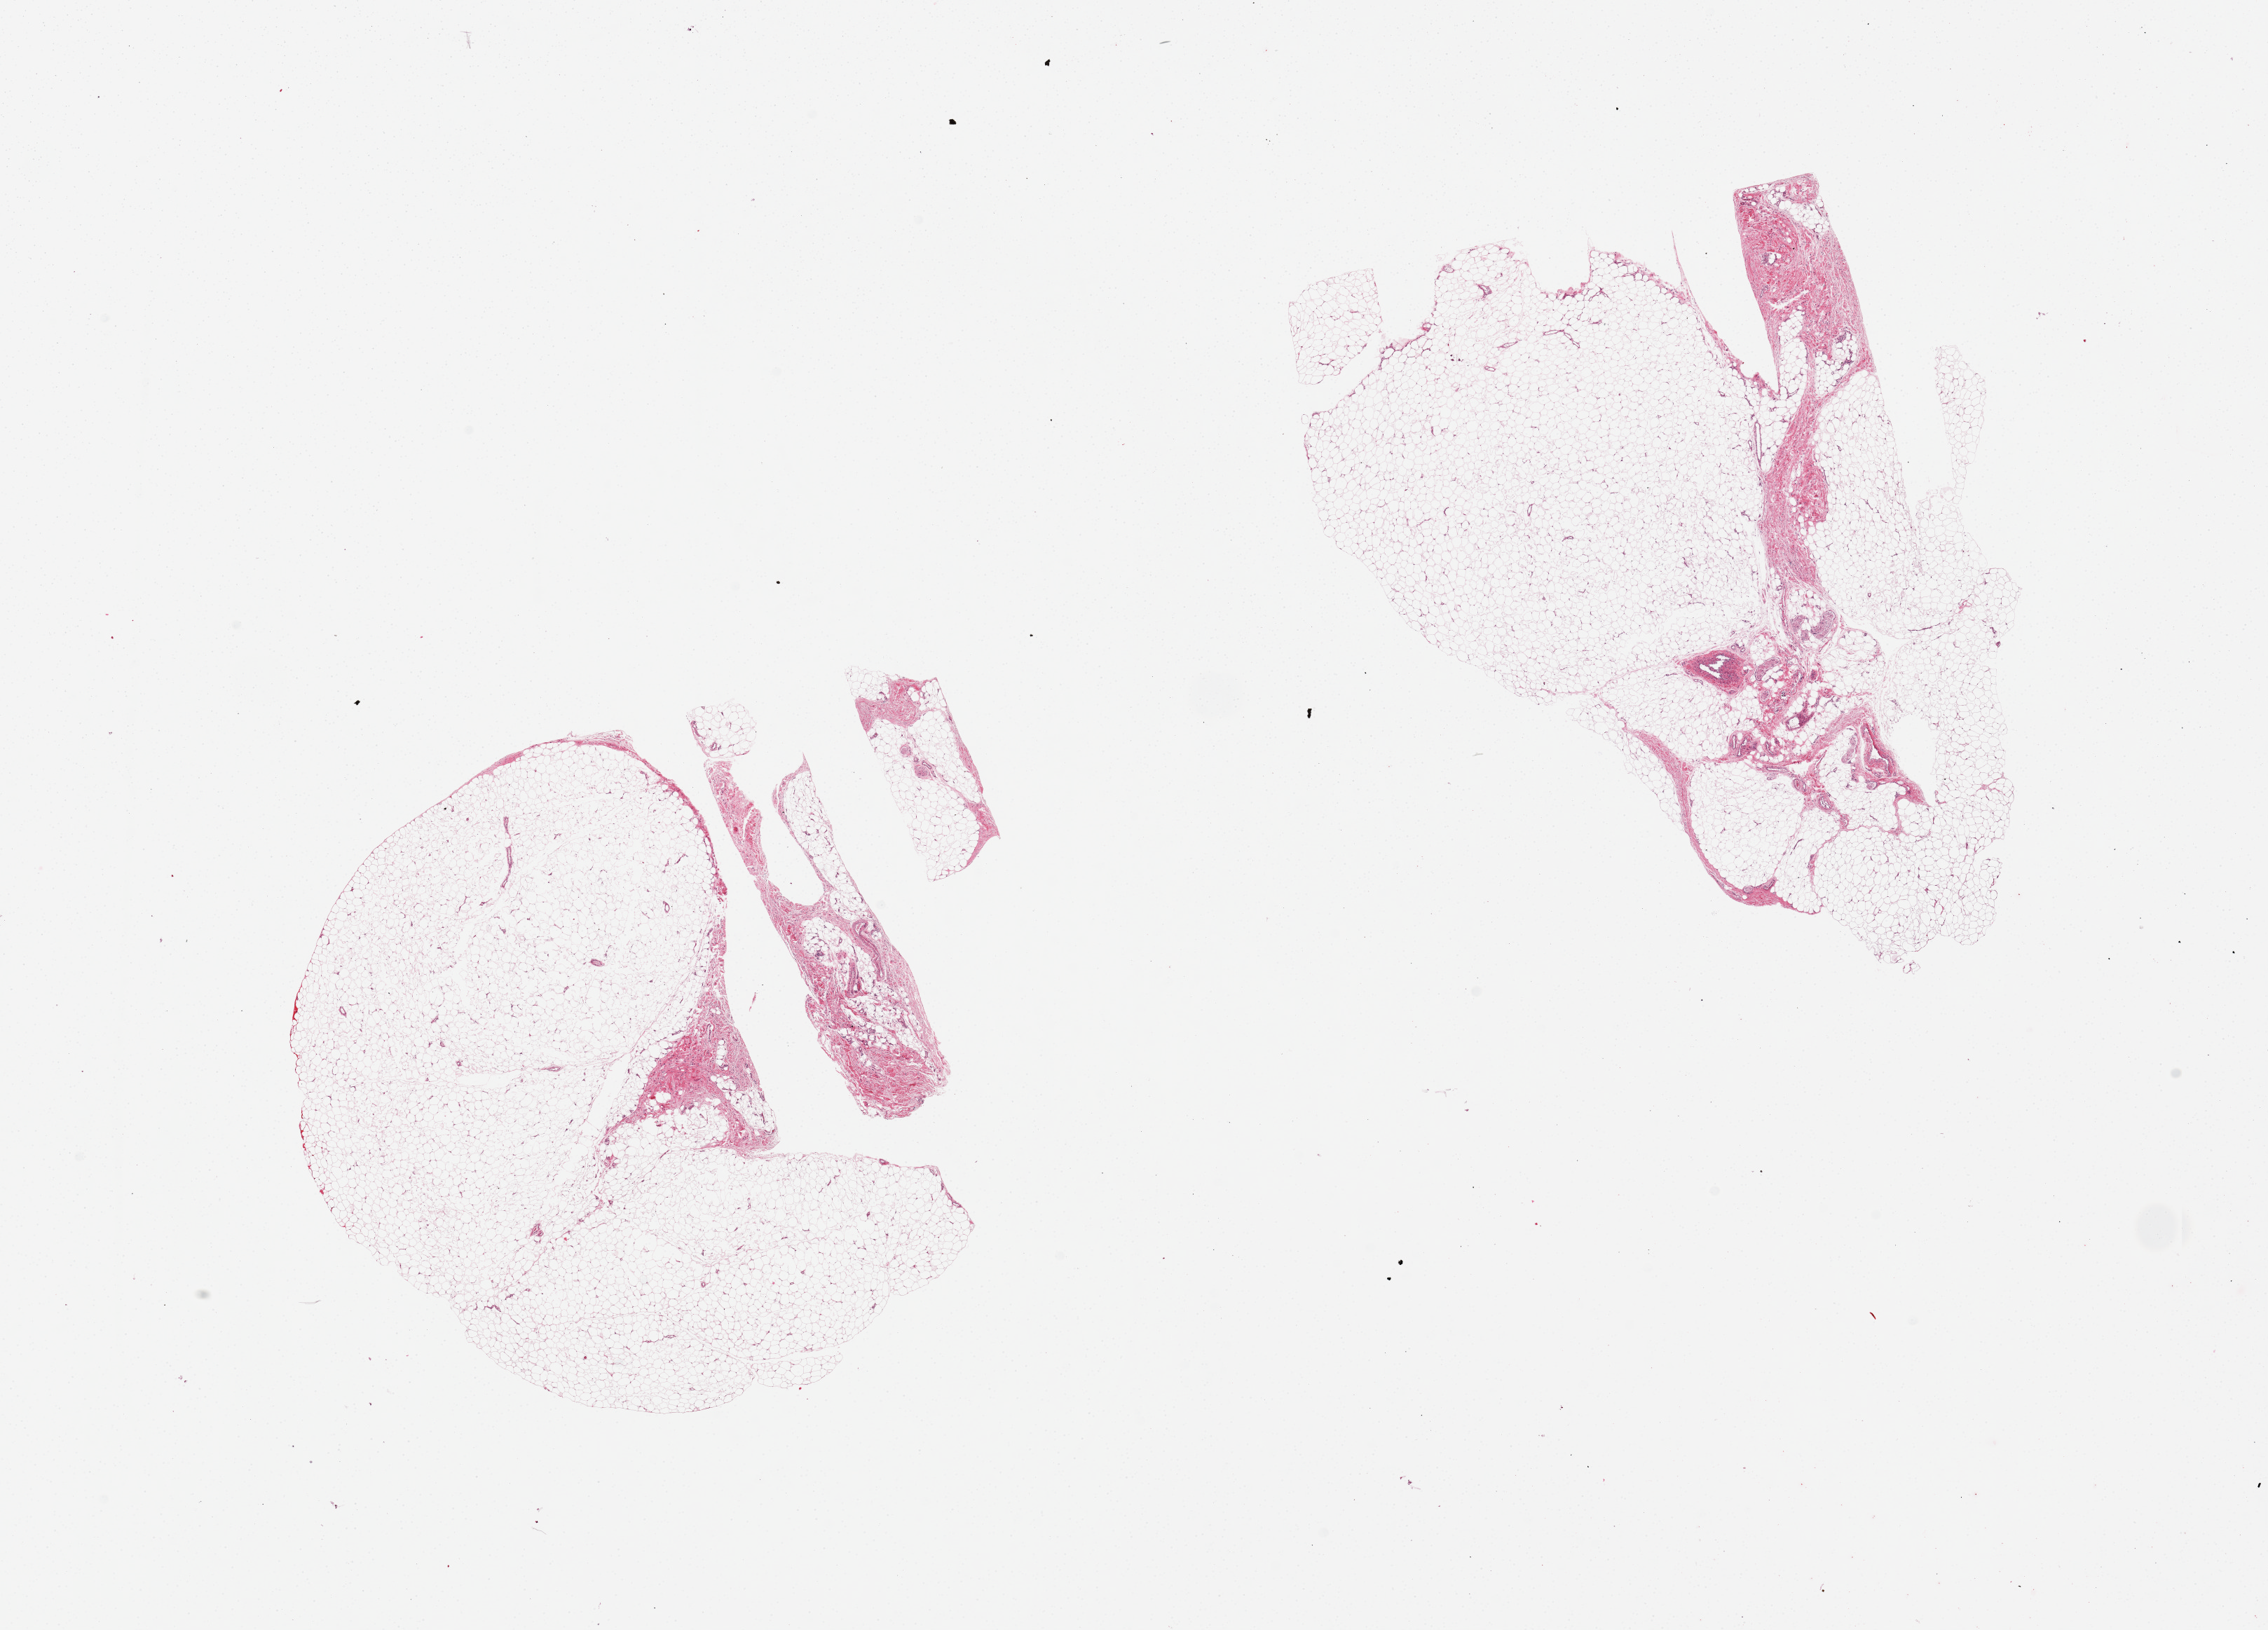
Whole-slide image, H&E stain, brightfield, shown as a low-resolution overview of the whole scanned area (about 25.6 x 18.4 mm, acquisition: 20x scan), PAXgene-fixed, paraffin-embedded tissue, section of adipose tissue (target tissue), tissue donor sample. Donor sex: female.
Review note (as recorded): 2 pieces, ~10% fibrous tissue.